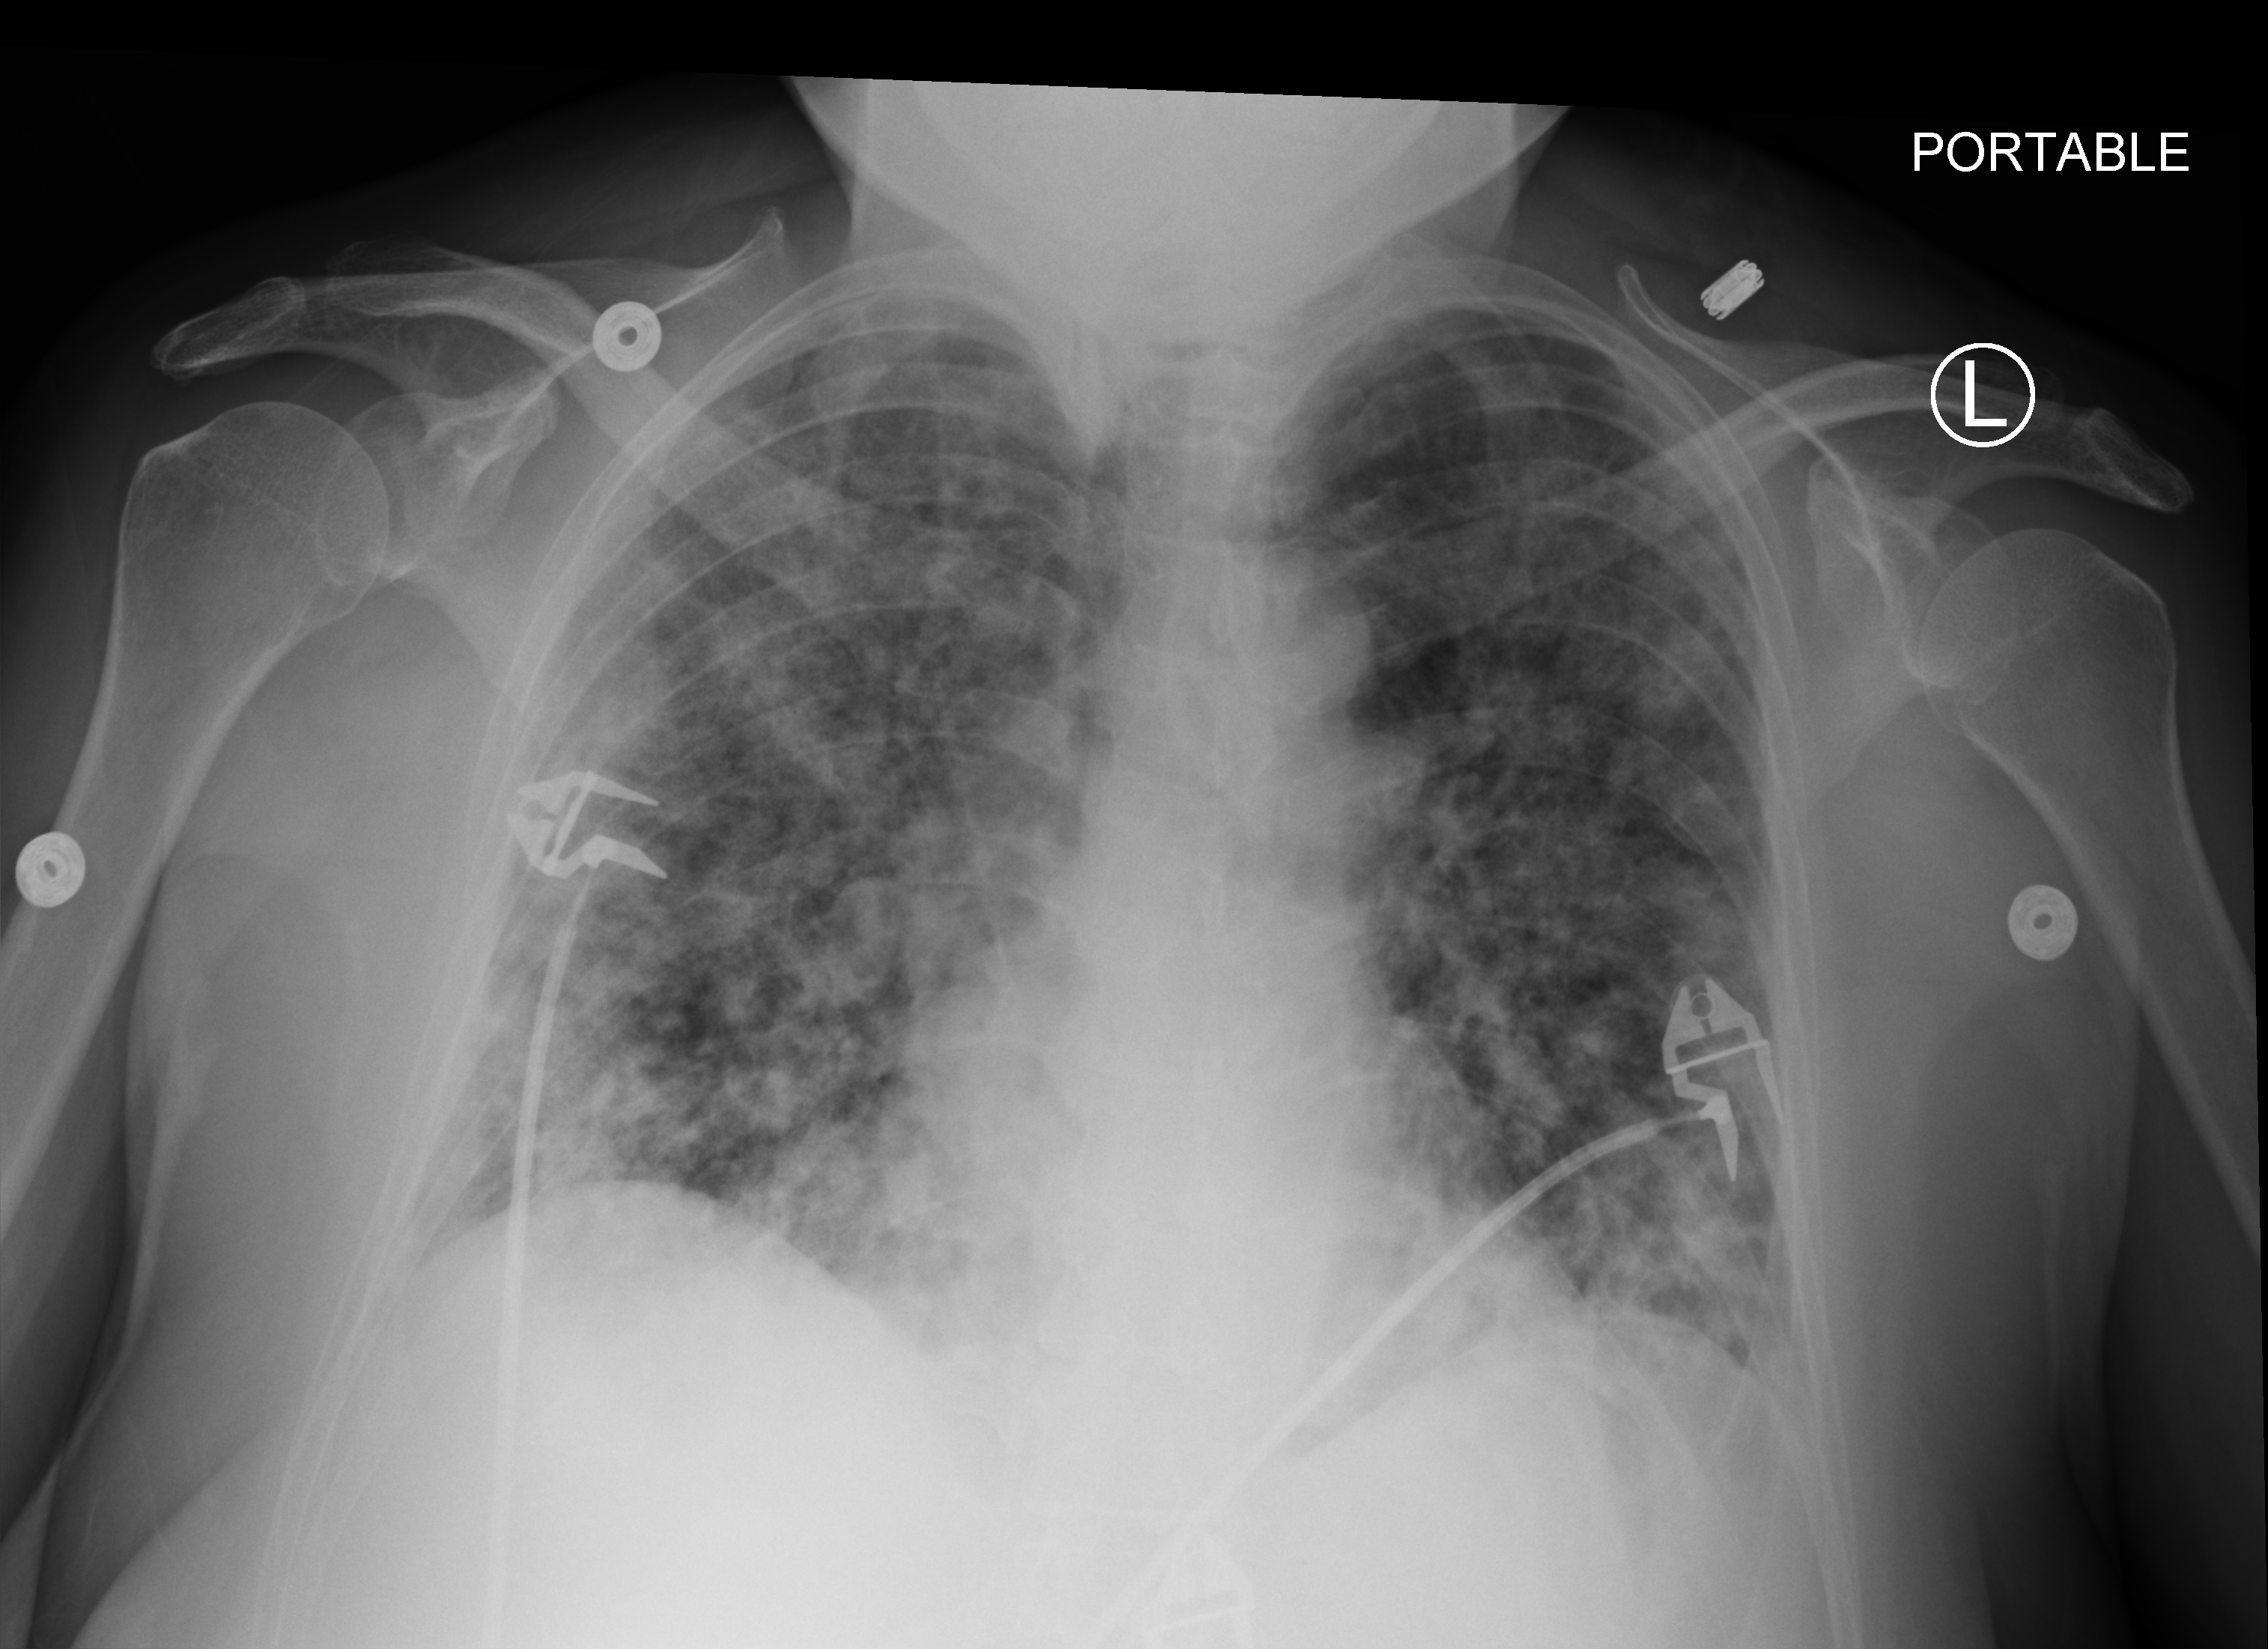
Portable chest radiograph; anteroposterior (AP) projection. Female patient hospitalised with COVID-19, age 60–74 years.
From the hospital-stay record, not from the radiograph (when in the stay this image was taken is not recorded): mechanically ventilated during this hospital stay: no.